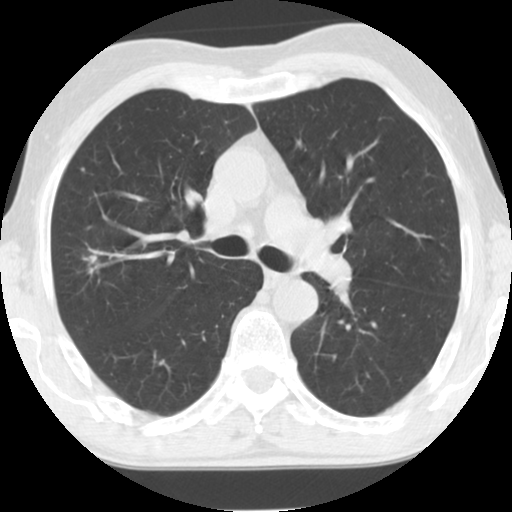
Chest CT (low-dose screening protocol), one axial image. Second screening round (one year after baseline). Lung window (W 1500 / L -600 HU). 2.5 mm slice thickness. Standard (soft-tissue) reconstruction kernel (STANDARD). 512 × 512 image matrix, field of view 310 × 310 mm. Male participant, aged 69 years at enrolment. Former smoker at enrolment.
• Expert-annotated lung lesion, box from (x=67, y=226) to (x=125, y=292) px.
• Screening reader's record for this exam (one nodule recorded; not confirmed to be the boxed lesion): non-calcified nodule or mass ≥4 mm, right upper lobe, 12 × 8 mm, spiculated (stellate) margins, soft tissue attenuation, pre-existing on the prior screen: yes; interval growth: yes.
• Official screen result: positive, other.
• Later outcome: lung cancer diagnosed 196 days after this screen — mucinous adenocarcinoma, right upper lobe, moderately differentiated (G2), stage IA (AJCC 6th edition), 11 mm at pathology.